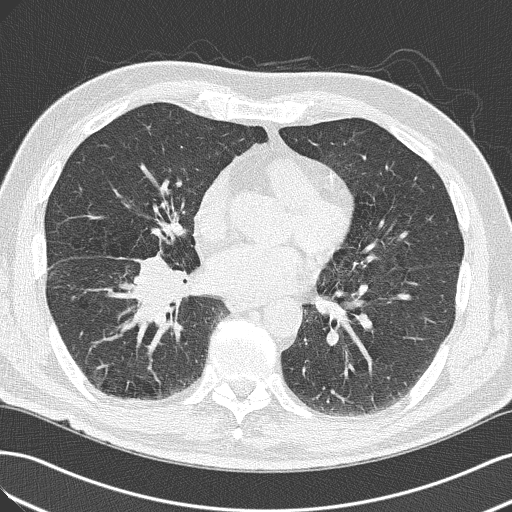
Low-dose screening chest CT, axial slice. Baseline screening round. Lung window (W 1500 / L -600 HU). Lung (sharp) reconstruction kernel (B50f). 120 kVp. Slice 88 of 143 in the series. Male participant, aged 65 years at enrolment. Current smoker at enrolment.
• Lesion marked by an expert reader, box from (x=103, y=251) to (x=206, y=340) px.
• The exam's reader record, not a measurement of the box and not confirmed to be the same lesion: non-calcified nodule or mass ≥4 mm, right upper lobe, 18 × 13 mm, spiculated (stellate) margins, soft tissue attenuation.